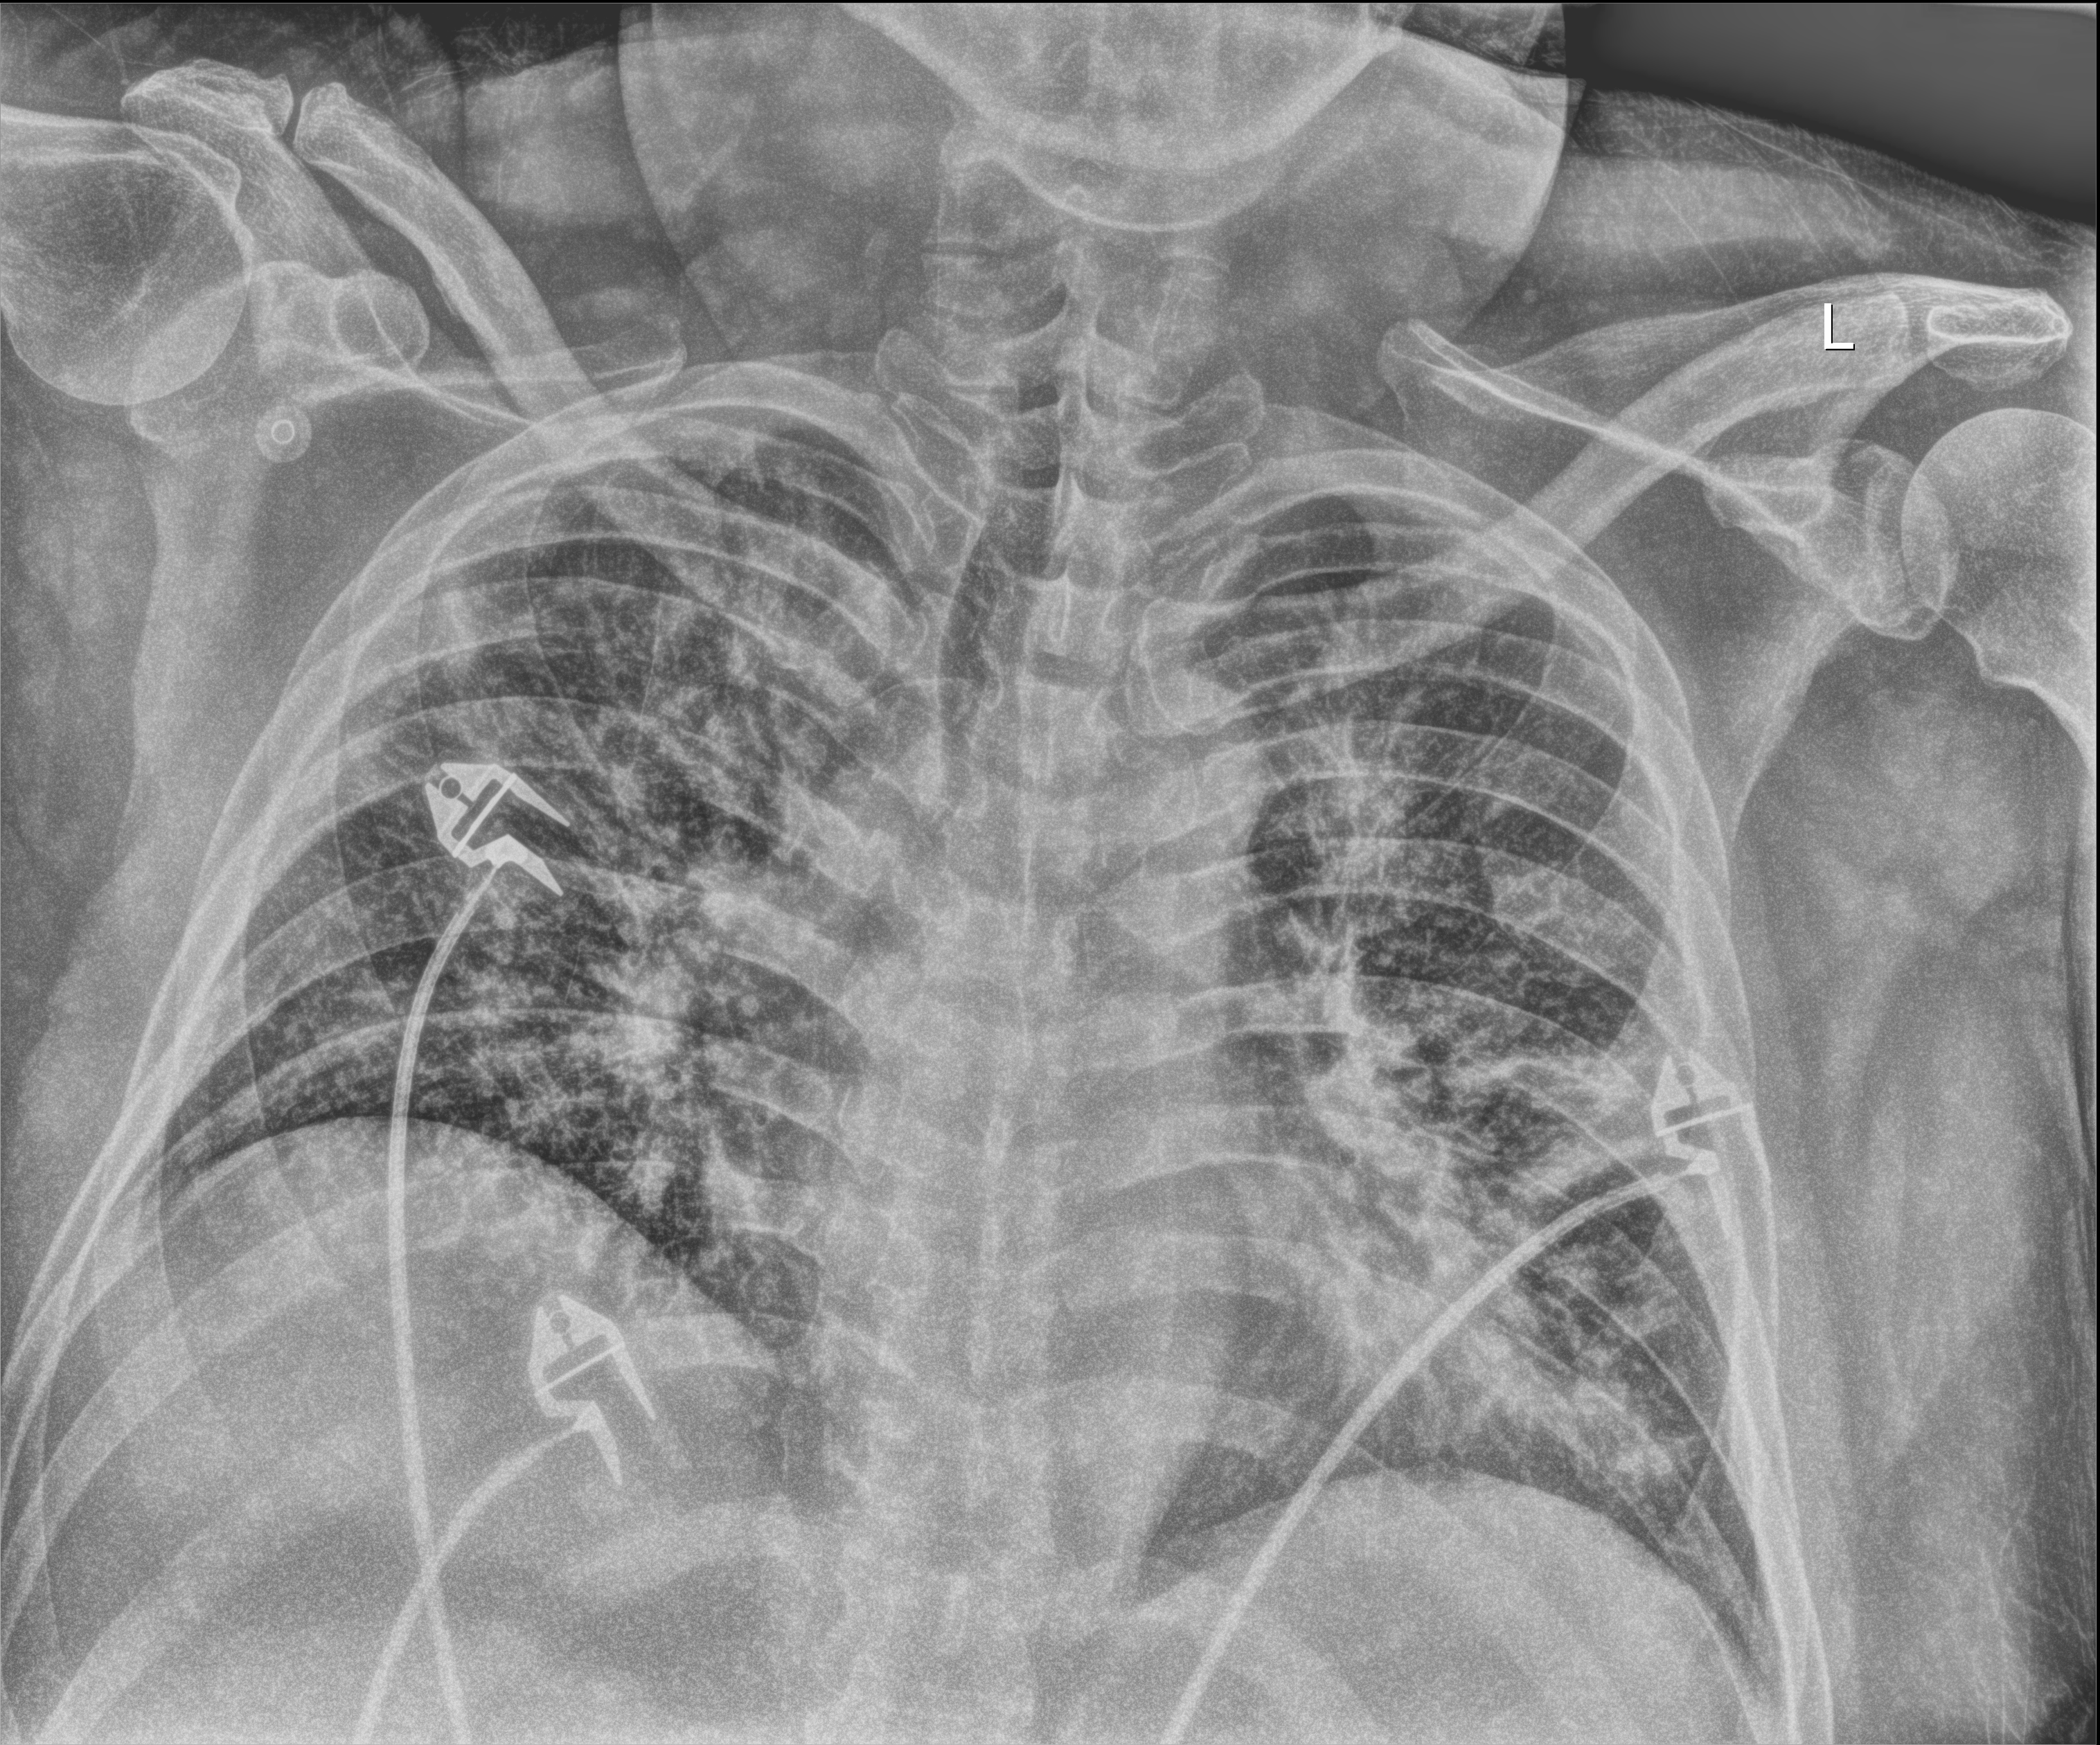
Chest X-ray (portable); anteroposterior (AP) projection. Male patient hospitalised with COVID-19, age 18–59 years.
Admission-level facts for this patient (not findings on this image; timing relative to this image not recorded): mechanically ventilated during this hospital stay: no.